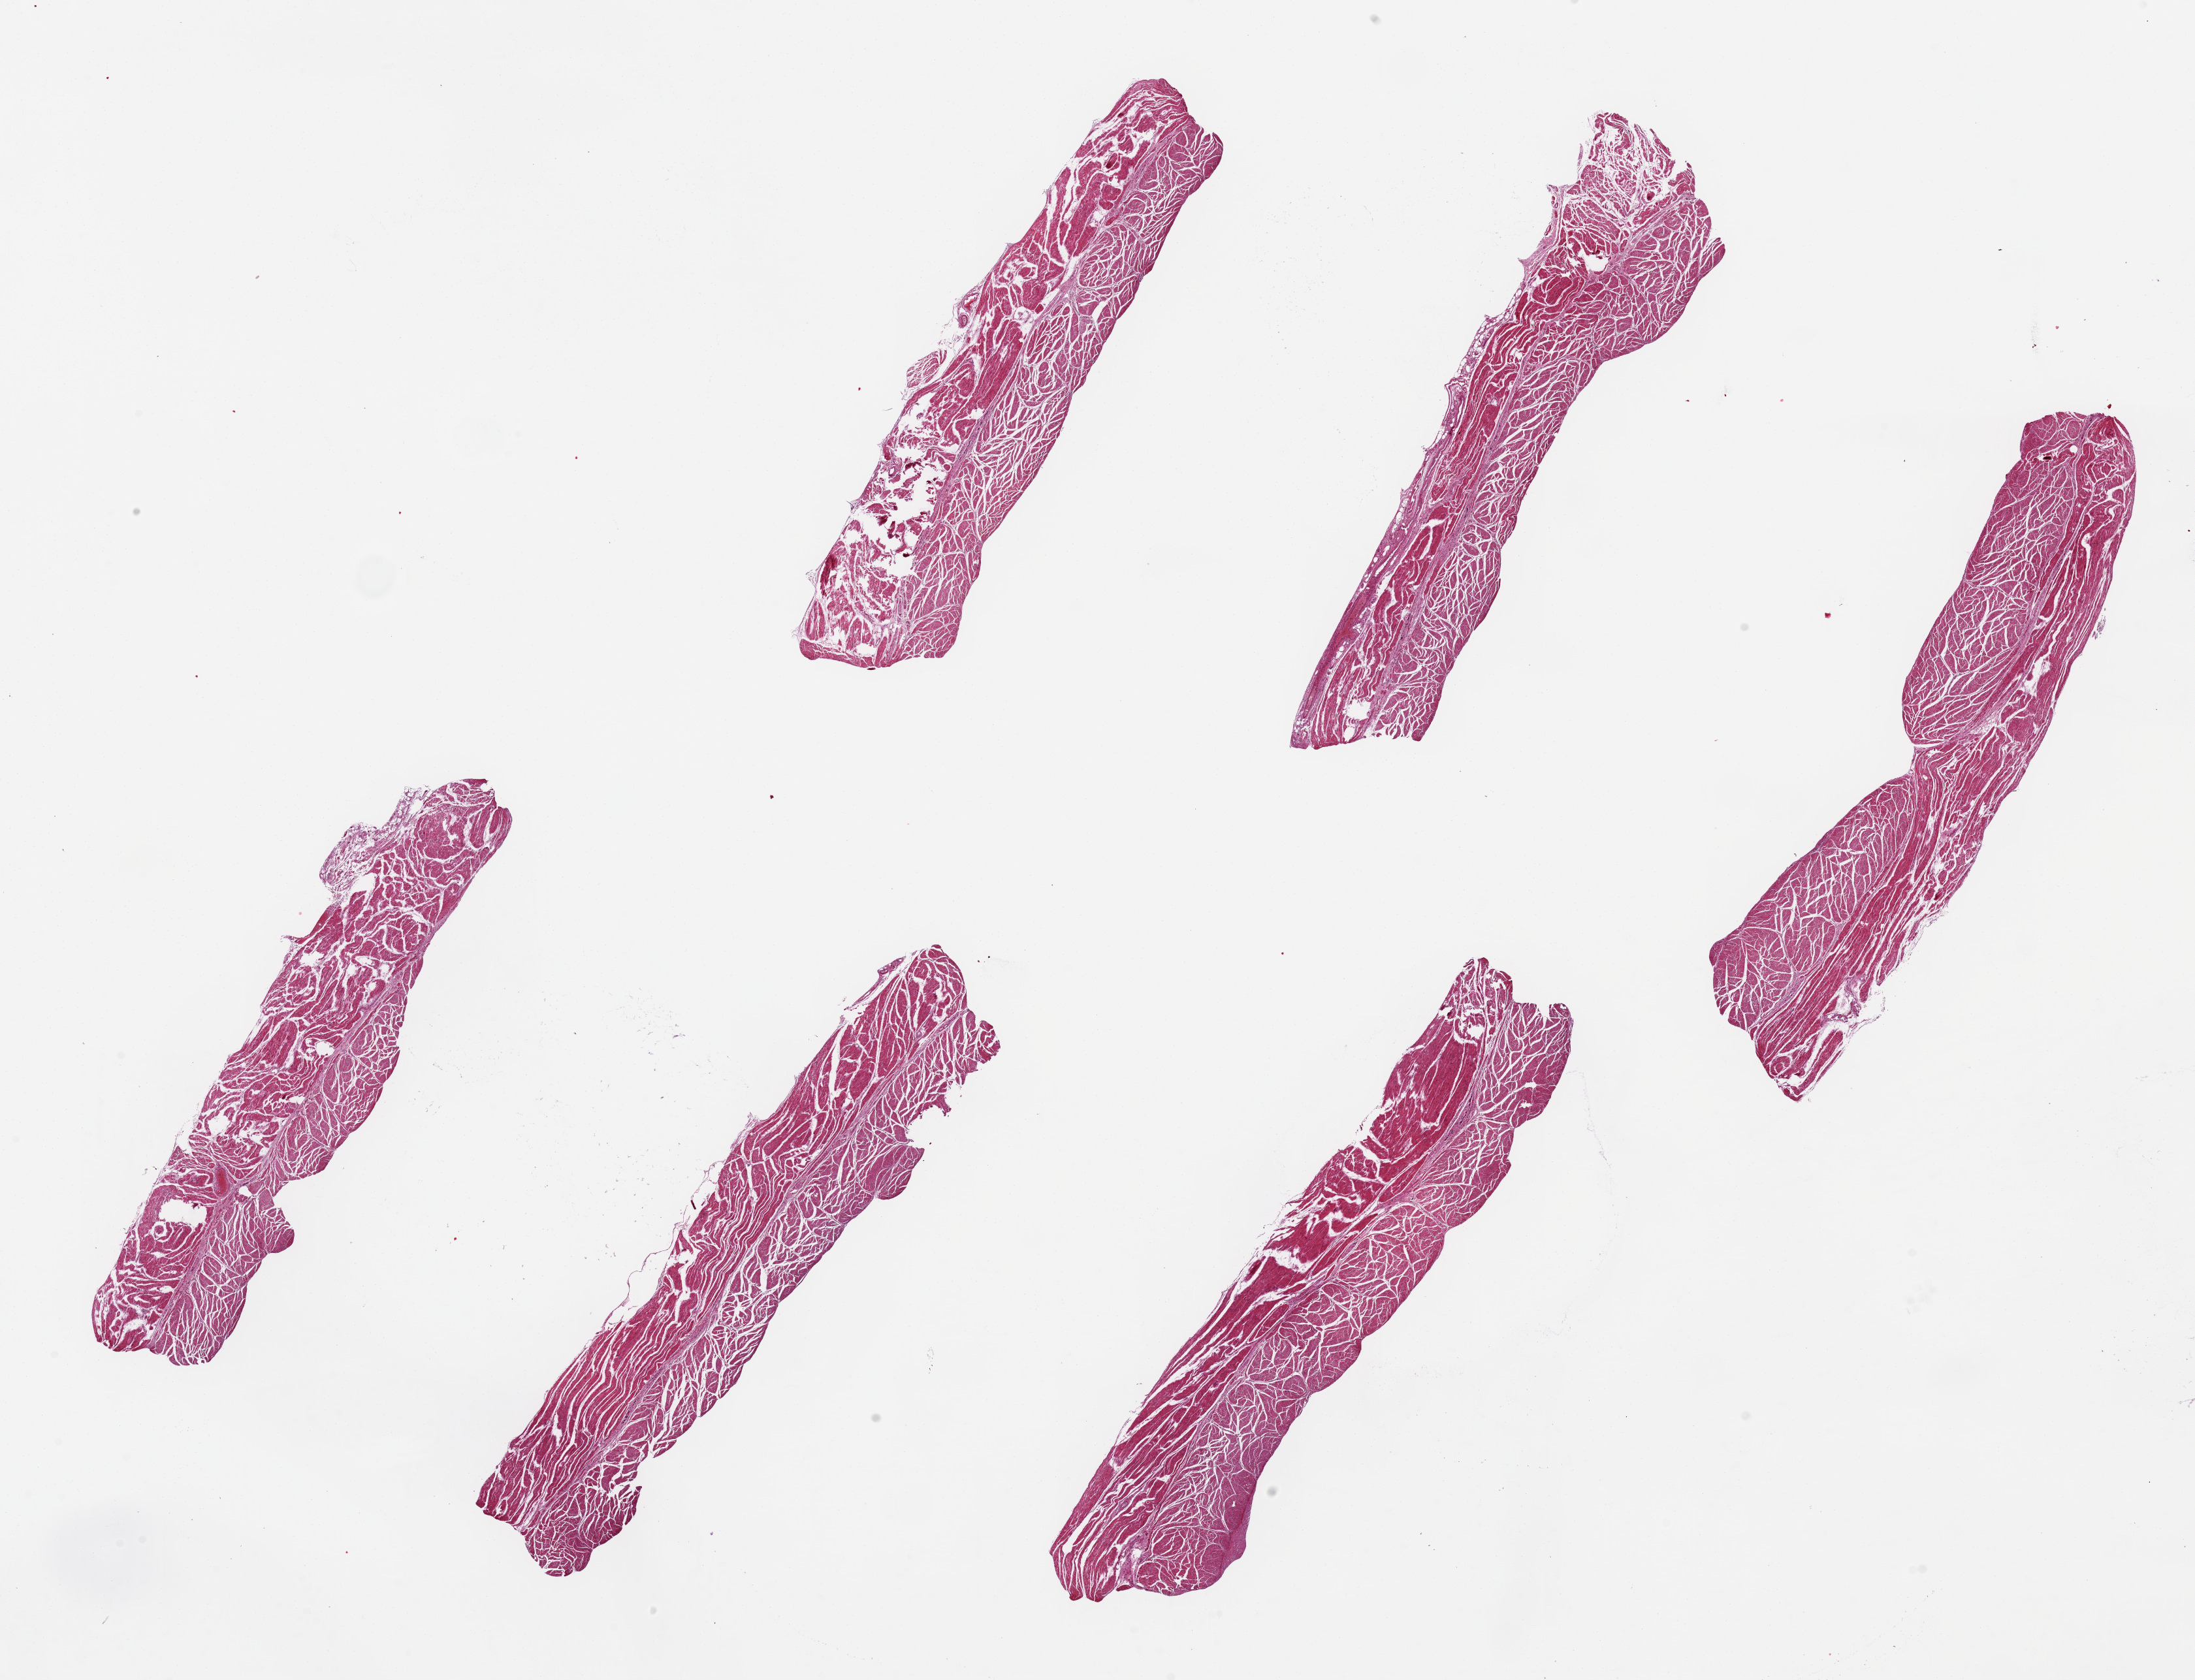
Digitized haematoxylin and eosin-stained section, brightfield — a low-resolution overview of the entire scanned area, about 26.6 x 20.3 mm. PAXgene-fixed paraffin-embedded (PFPE) section. Sampled site (target tissue): esophageal muscle. Tissue donor sample.
* review note (as recorded): 6 pieces up to 9x2 mm